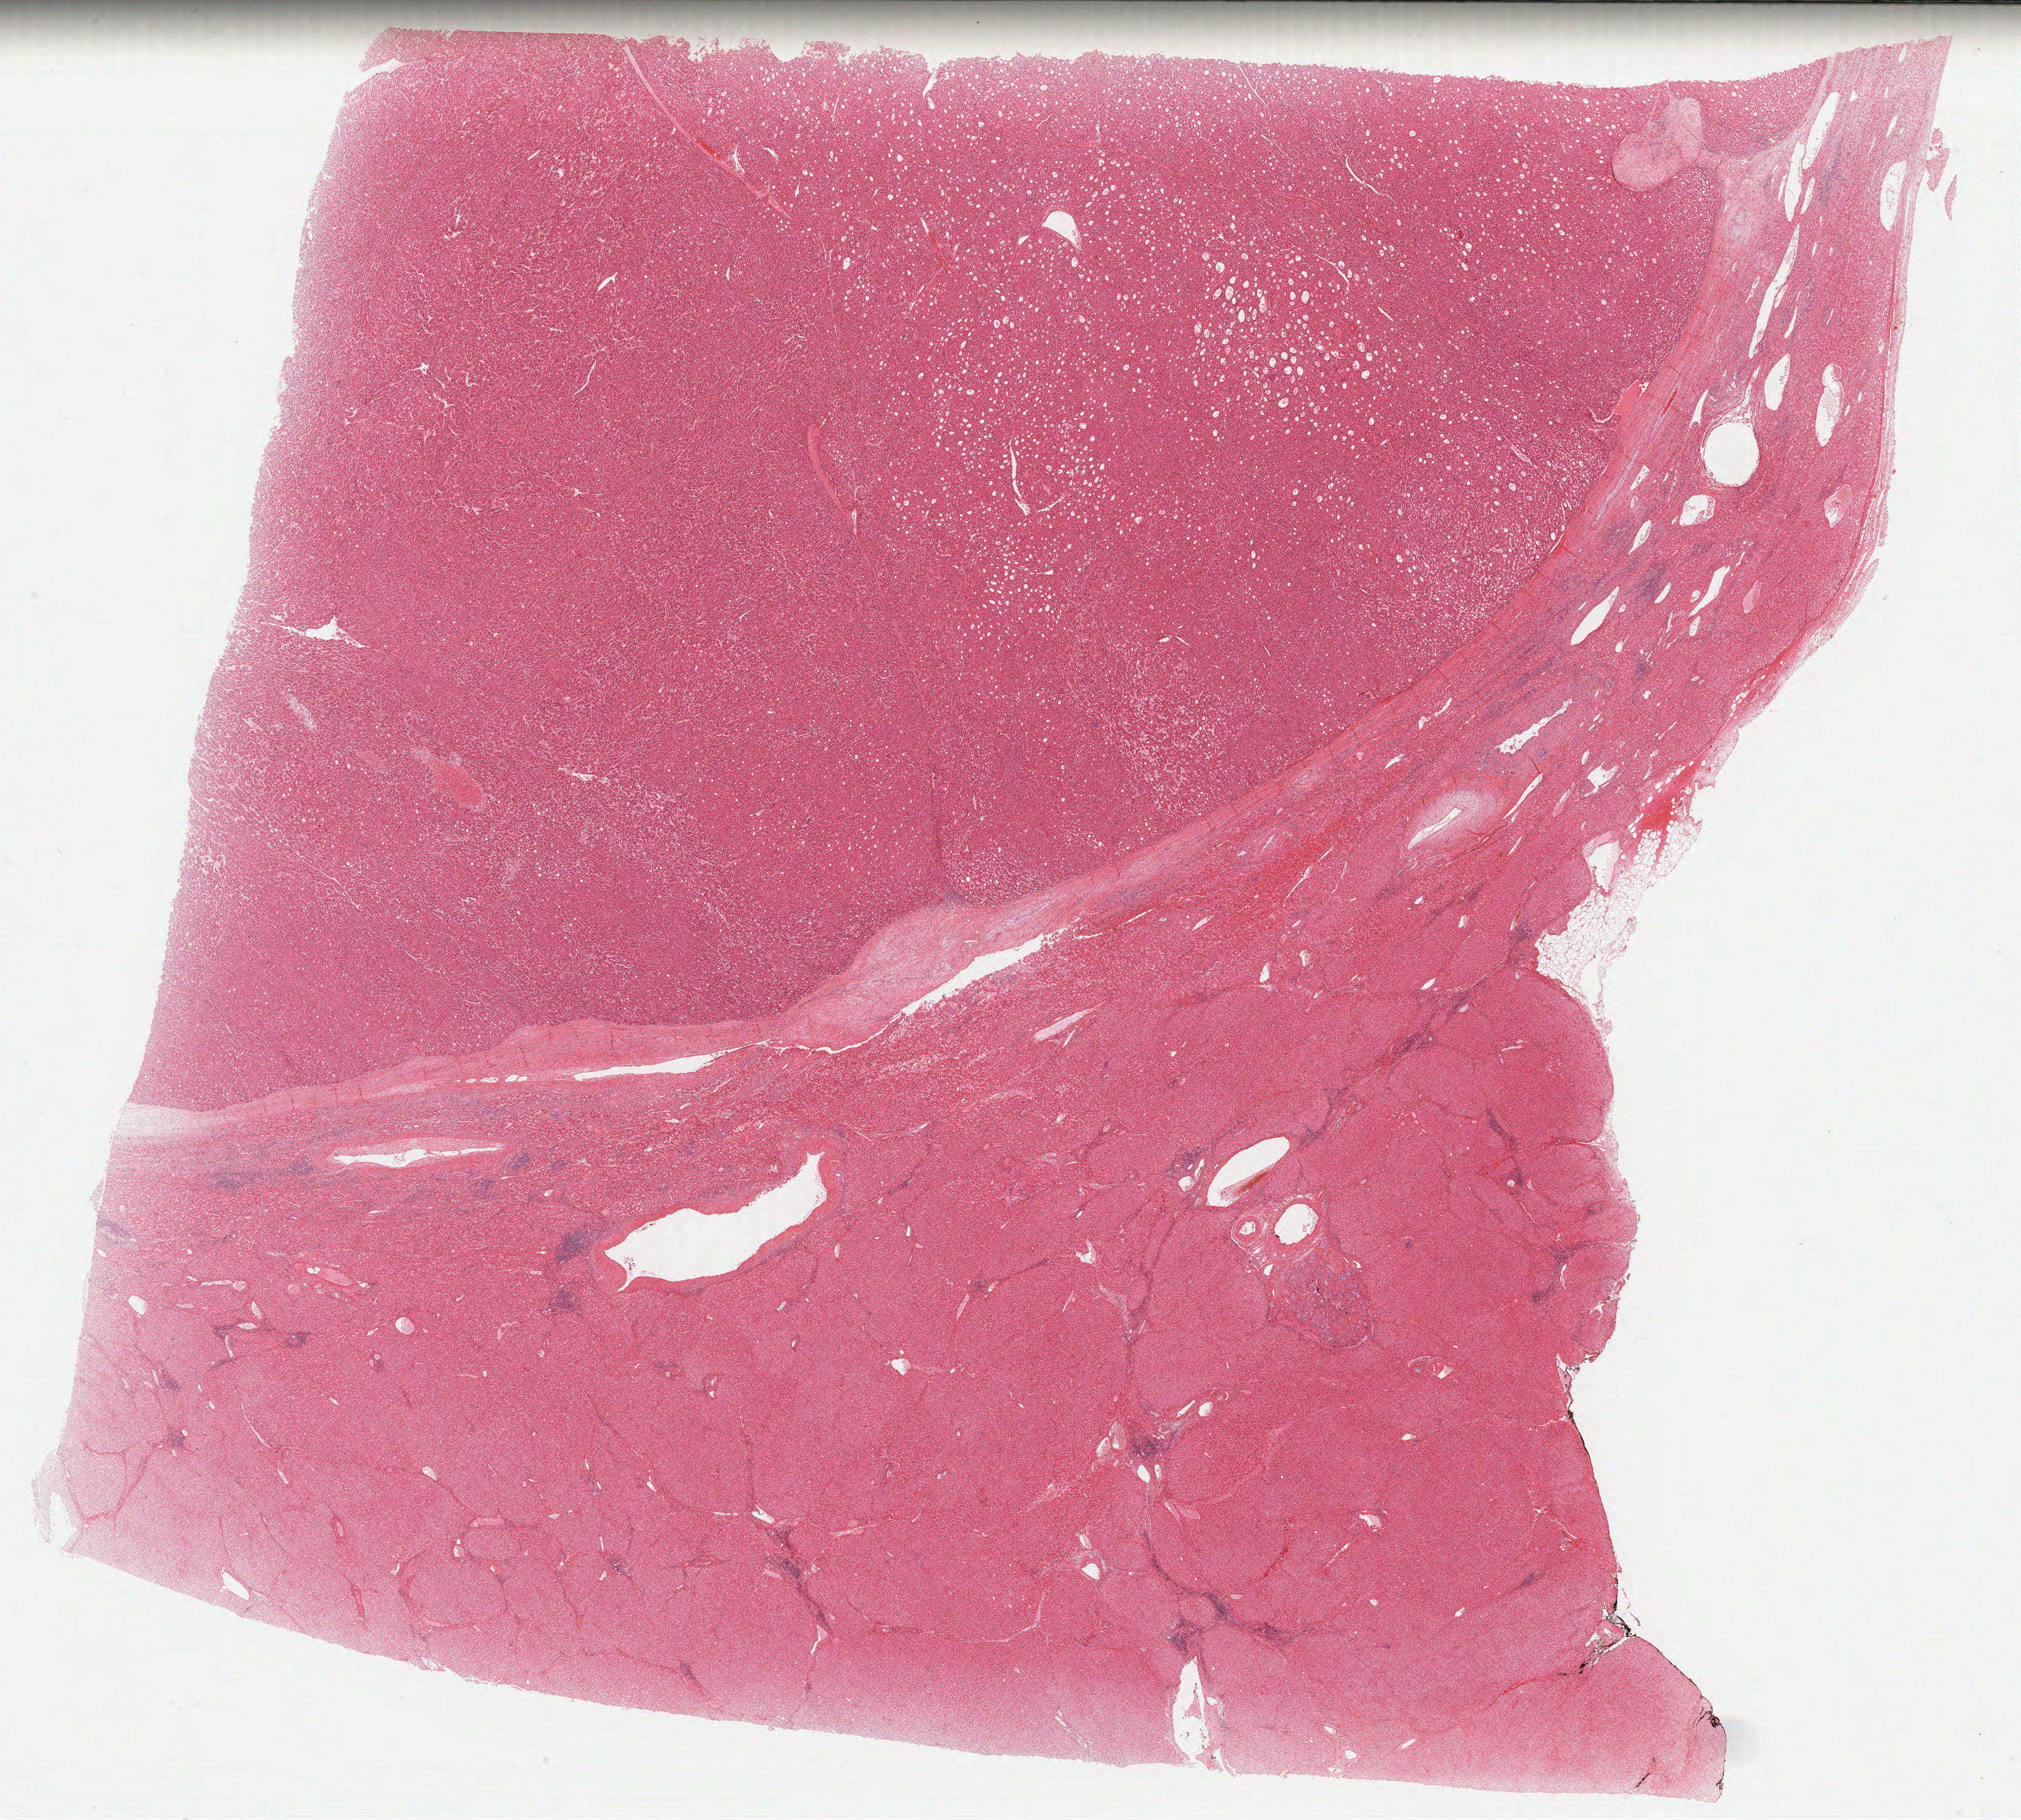
Digitized Hematoxylin and eosin (H&E) stained tissue section (whole slide), low-resolution overview of the scanned area, about 26.1 x 23.5 mm, formalin-fixed paraffin-embedded (FFPE) diagnostic section, liver, primary tumour sample. Male, age 69 years at initial diagnosis. Histologic grade: G2 (moderately differentiated).
Pathologic diagnosis: Hepatocellular carcinoma, NOS. TNM: T1 N0 M0. AJCC pathologic stage: I (6th edition).